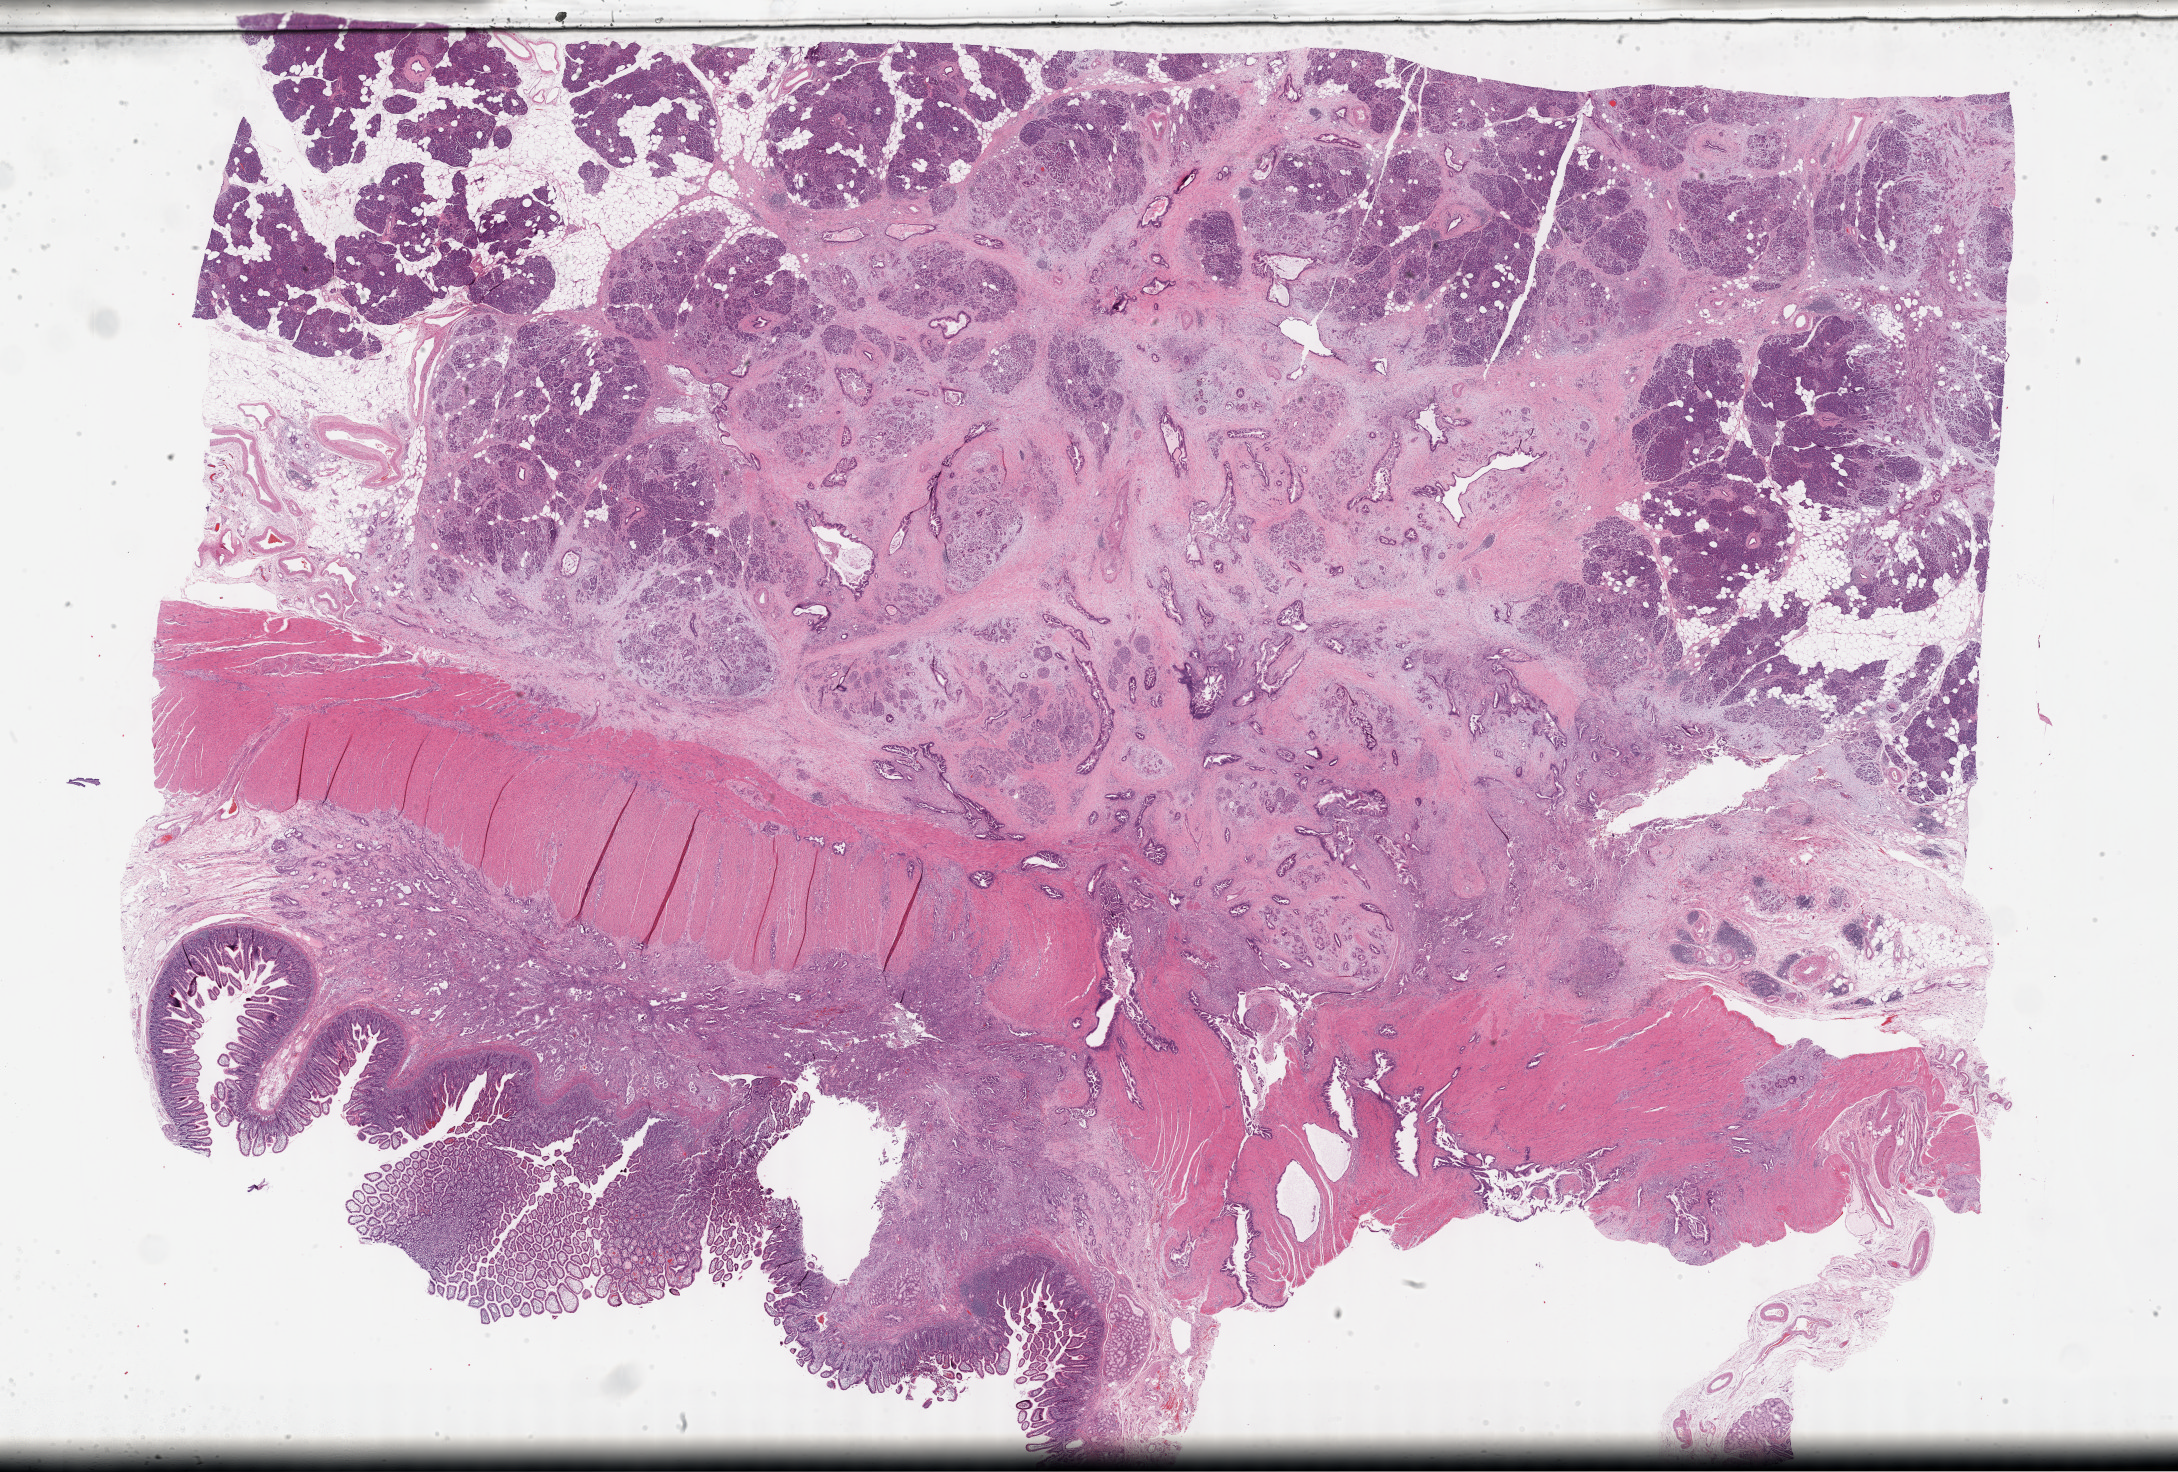
Whole-slide histology image, H&E — shown as a low-resolution overview of the whole scanned area (about 35.2 x 23.8 mm, from a 40x scan). Formalin-fixed paraffin-embedded (FFPE) diagnostic section. Sample: primary tumour, pancreas. Female, age 77 years at initial diagnosis. Histologic grade: G3 (poorly differentiated).
• TNM: T3 N1 MX
• AJCC pathologic stage: IIB (7th edition)
• lymph nodes positive (case pathology): 2 of 10 examined
• diagnosis: Infiltrating duct carcinoma, NOS